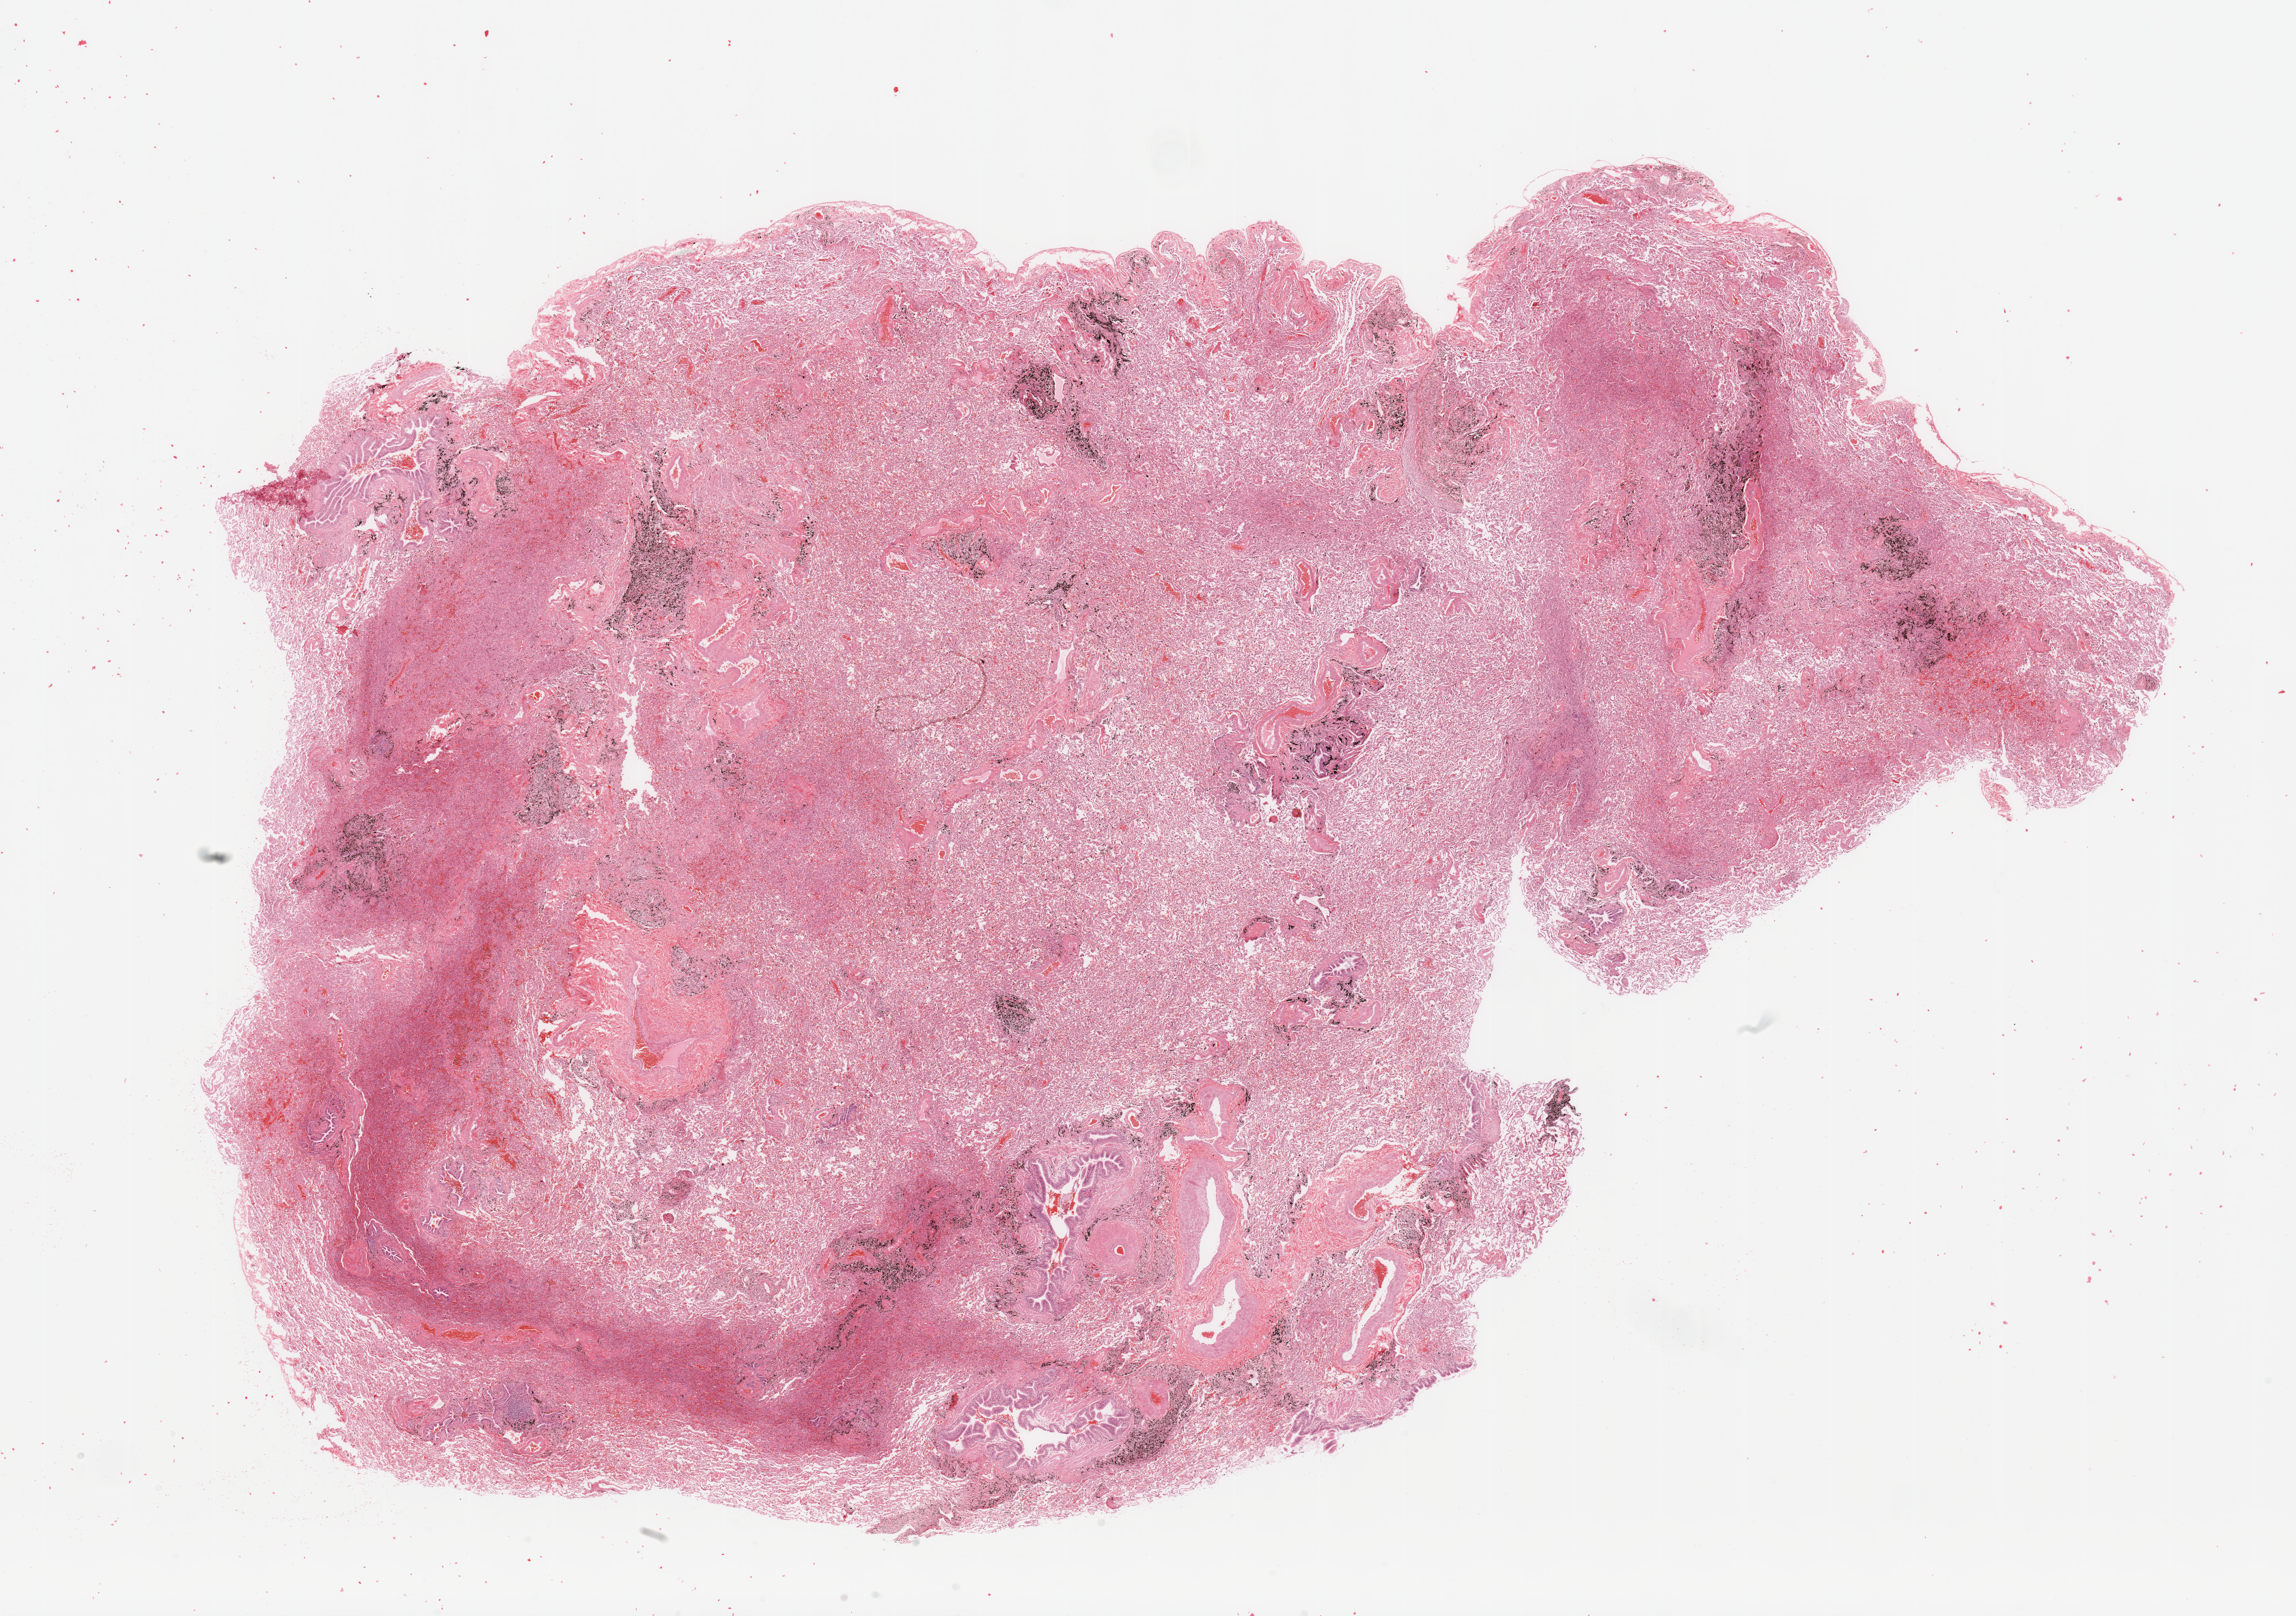
Digitized Hematoxylin and eosin (H&E) stained tissue section (whole slide) — shown as a low-resolution overview of the whole scanned area (about 26.6 x 18.7 mm, from a 20x scan). Normal (non-tumour) tissue sample, lung. Male, 64 y/o.
This section: normal (non-tumour) tissue from the same patient. Patient diagnosis: Adenocarcinoma, NOS.